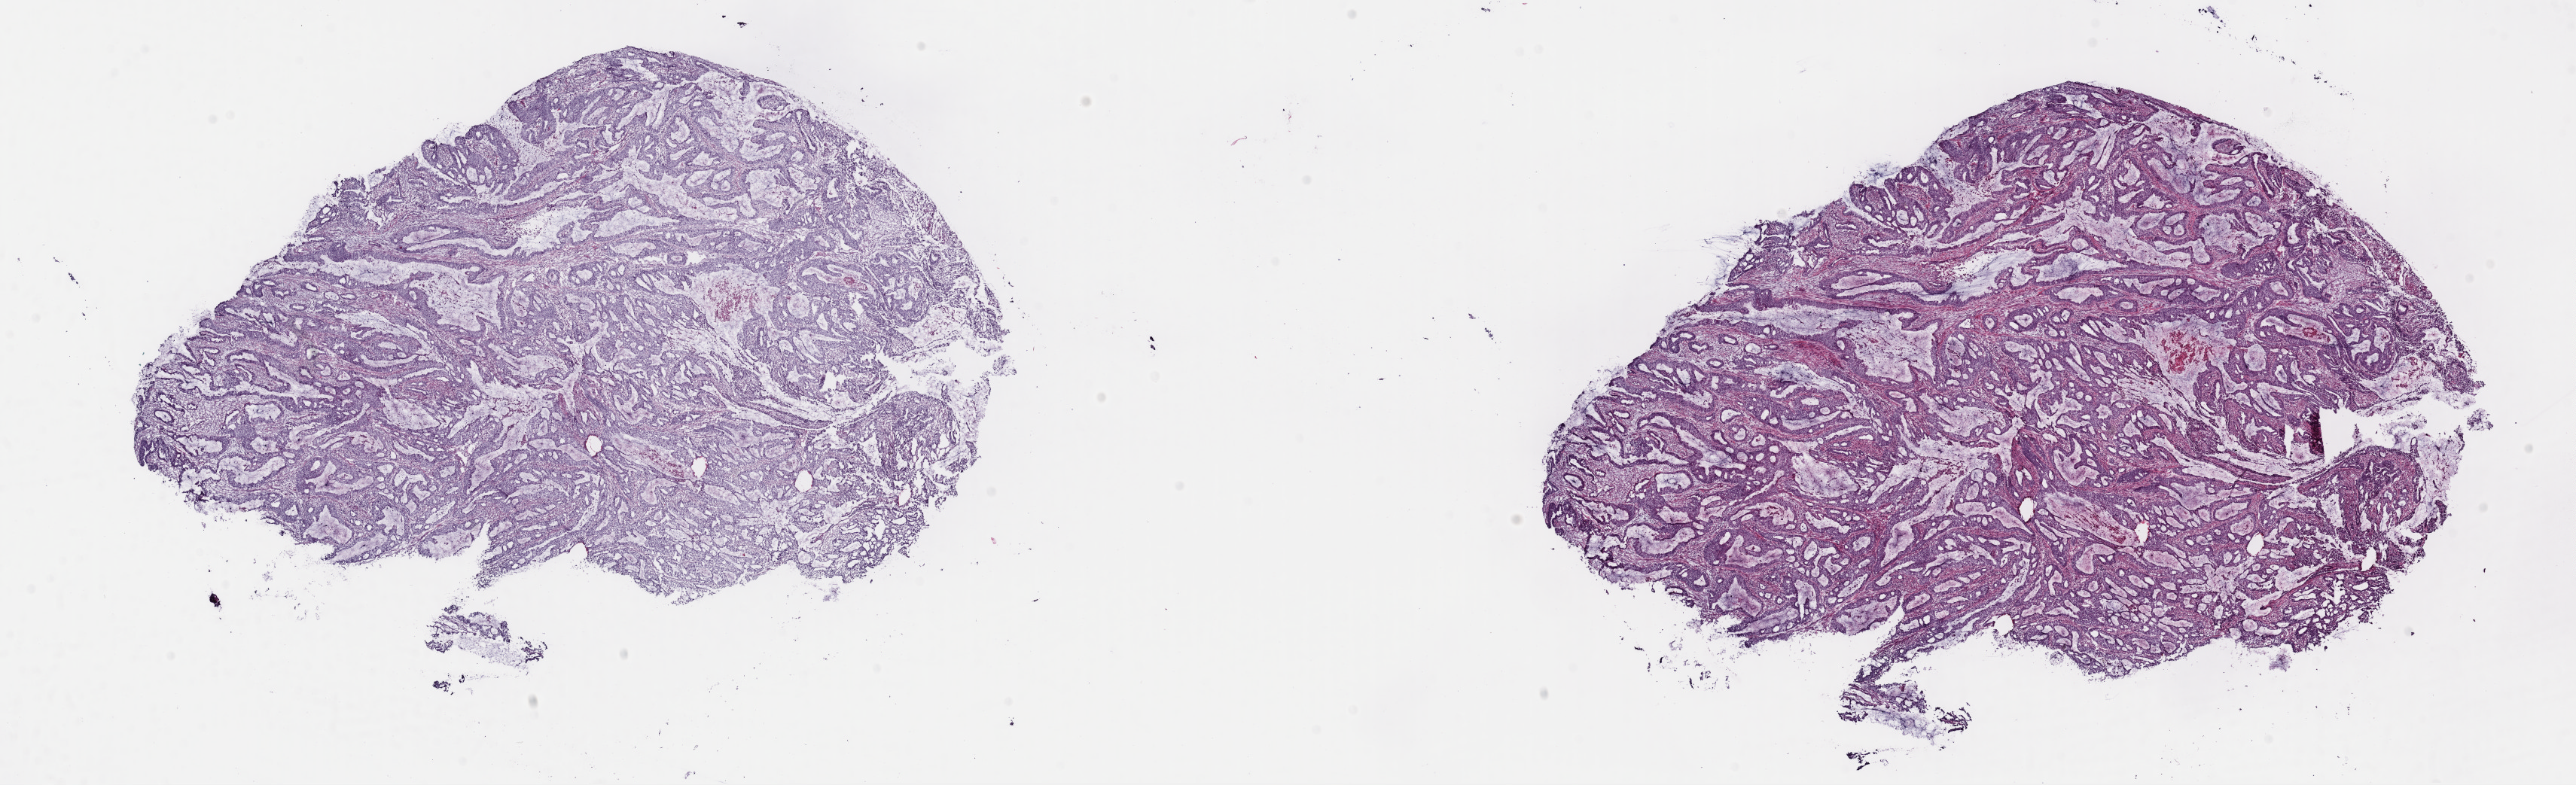
Digitized H&E-stained tissue section (whole slide), a low-resolution overview of the entire scanned area, about 27.0 x 8.2 mm (slide scanned at 40x); frozen section; primary tumour sample from the uterus. Female patient; age at initial diagnosis 54 years. Histologic grade: G3 (poorly differentiated). Slide review estimates, as recorded: tumour cells 90%, tumour nuclei 80%, normal cells 5%, stromal cells 0%, necrosis 5%. Inflammatory infiltration, as recorded: lymphocyte infiltration 5%, monocyte infiltration 1%, neutrophil infiltration 2%.
* FIGO stage: II
* diagnosis: Endometrioid adenocarcinoma, NOS (endometrium)